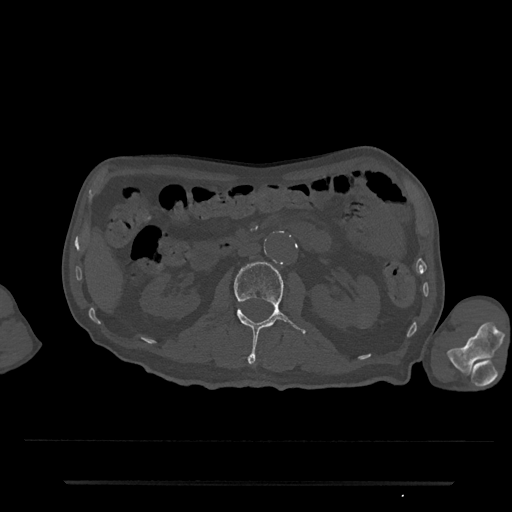
CT including the spine, one axial slice; reconstruction kernel Br40s/3; bone window (W 1800 / L 400 HU); 0.5 mm slice thickness; 512 × 512 image matrix, field of view 427 × 427 mm. Male patient, age 74 years. Case-level facts recorded for this patient, not image findings: primary cancer: prostate.
Annotated regions visible in this slice (semi-automatically segmented with operator editing):
- L2 vertebra: bounding box [x1, y1, x2, y2] px = [234, 262, 307, 363]